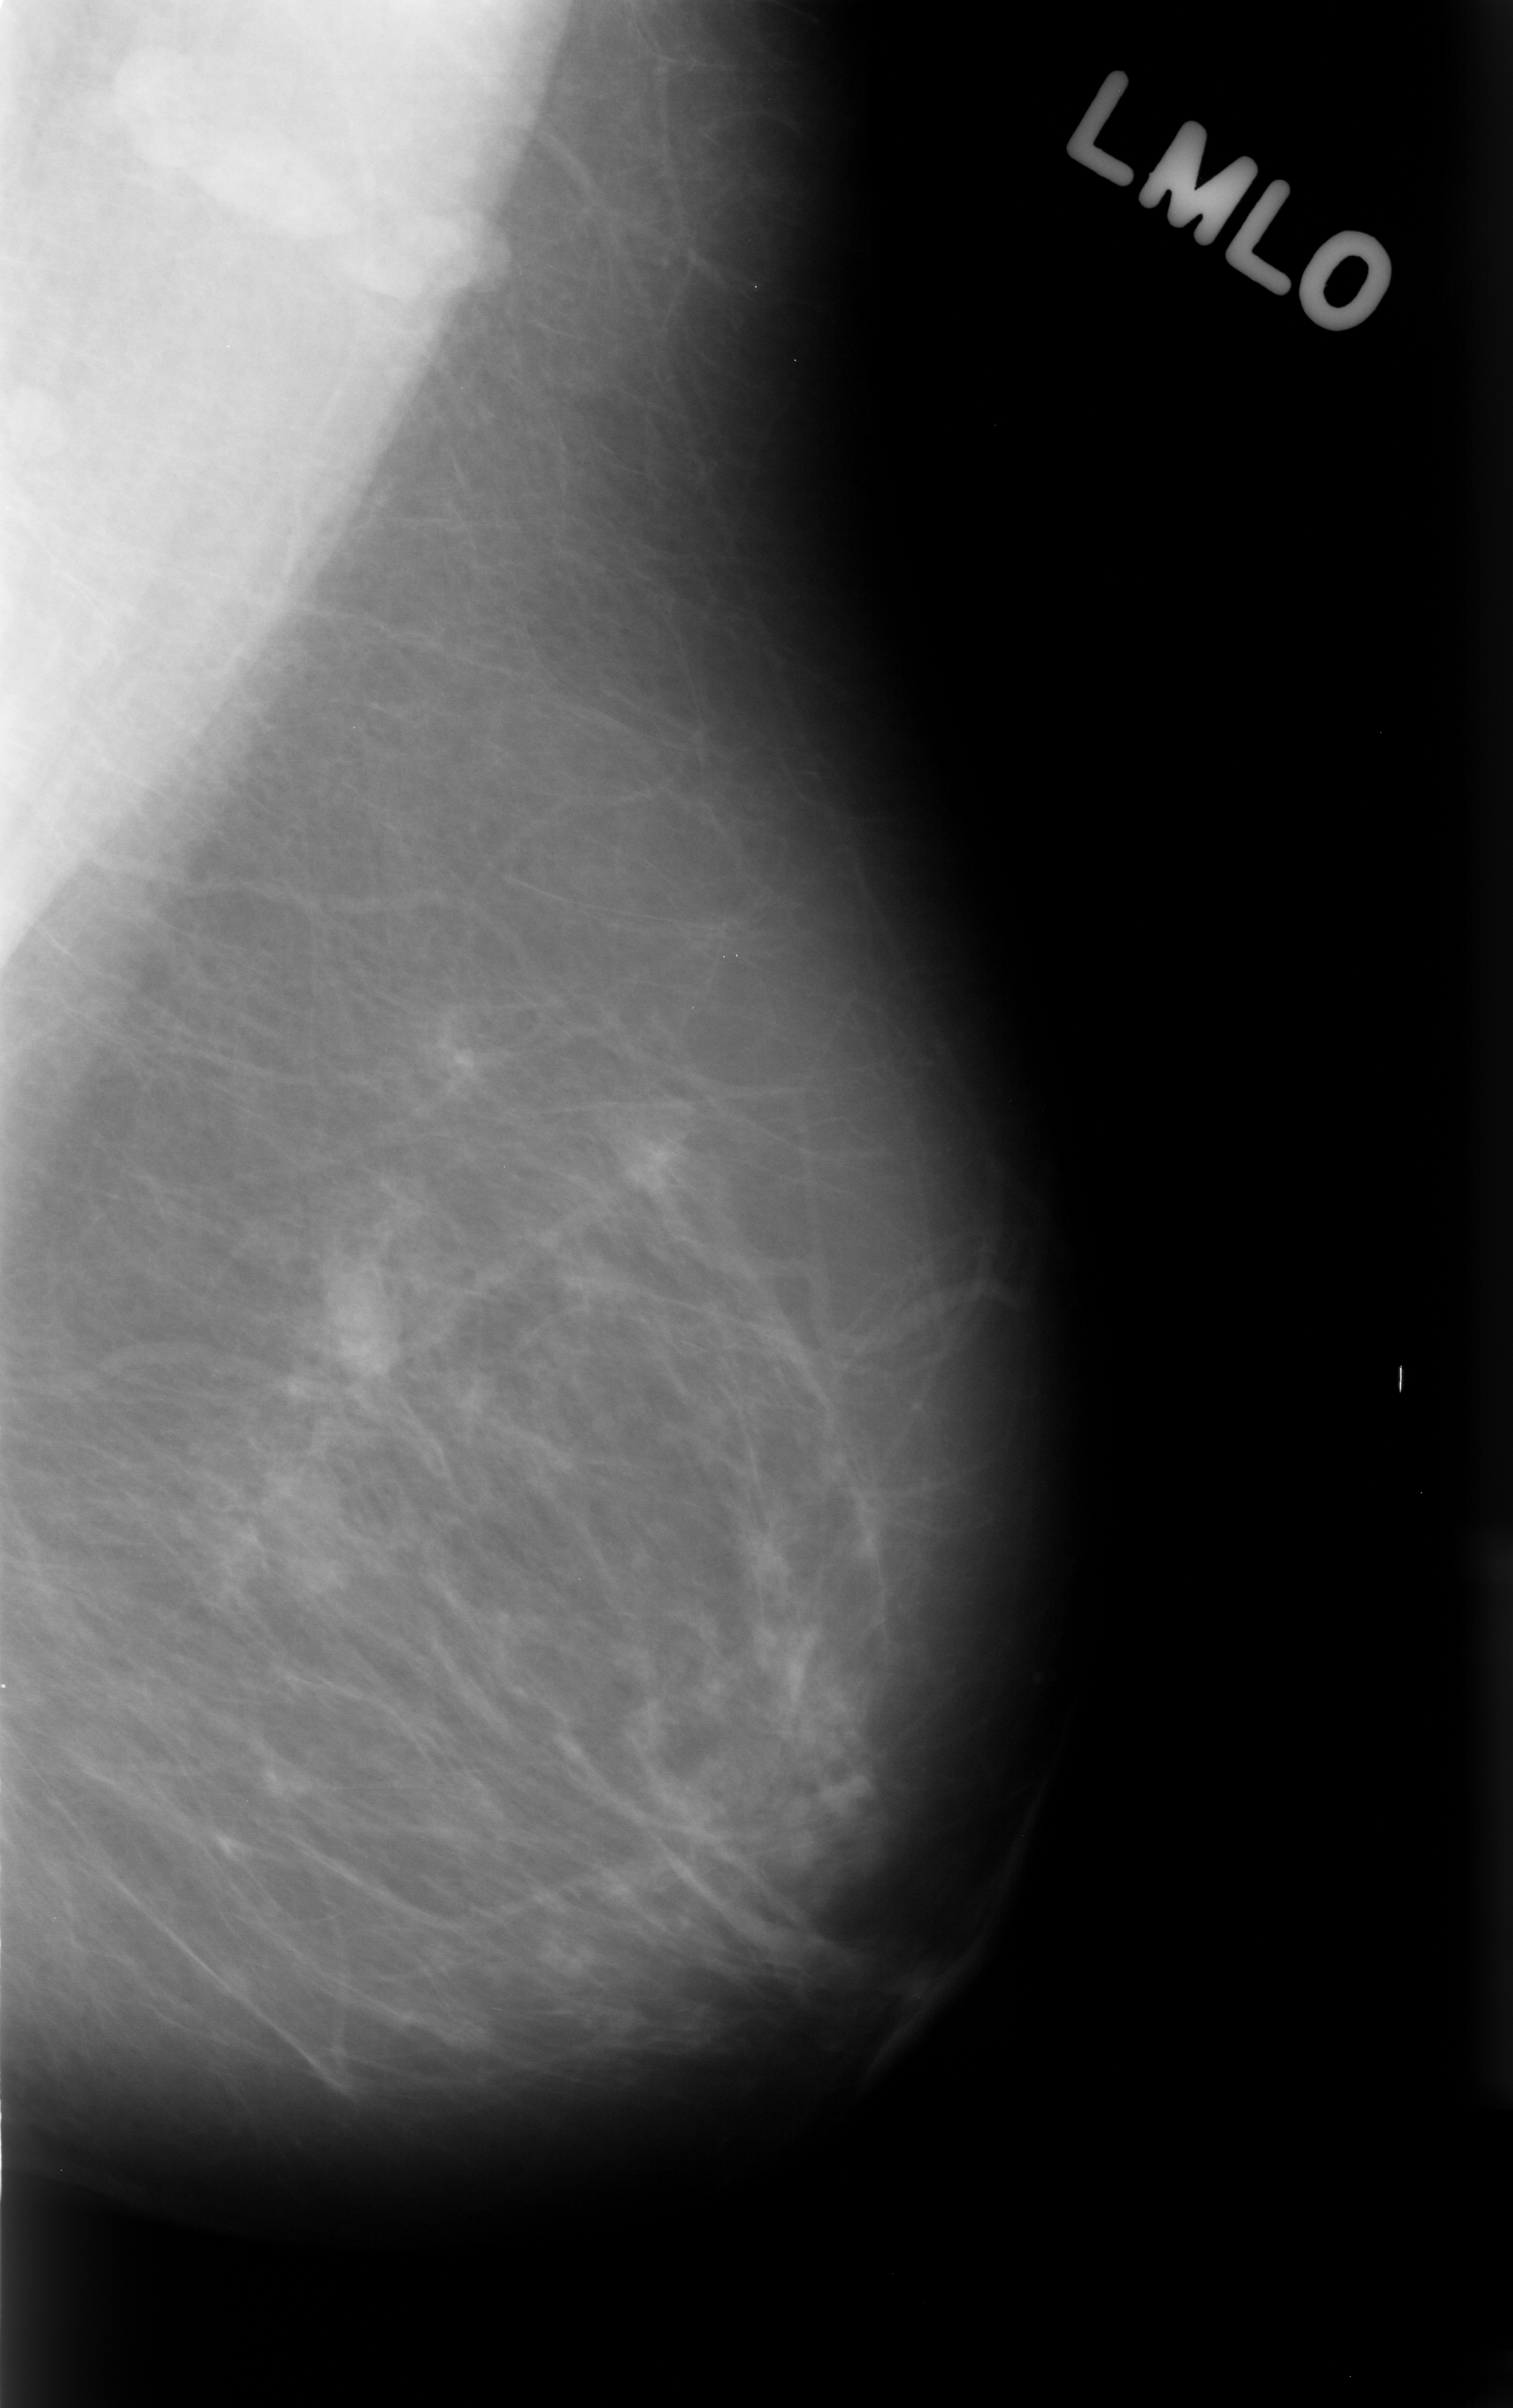
Digitized screen-film mammogram; left breast; mediolateral oblique (MLO) view; breast composition: almost entirely fatty (BI-RADS density category 1 of 4); 1513 × 2408 image matrix.
Expert-marked regions of interest on this image (one box per marked abnormality):
- mass, shape oval, margins circumscribed; BI-RADS assessment category 3; subtlety rating 5 on a 1 (subtle) to 5 (obvious) scale; benign; no additional work-up was recommended (outcome (as recorded, no biopsy): benign without callback): box from (x=293, y=1218) to (x=428, y=1397) px